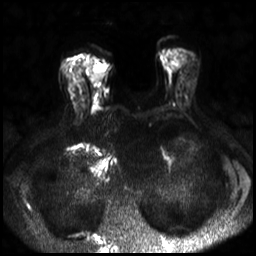
Breast MRI, one axial slice. Slice 11 of 30 in the series (ordered by position). Diffusion-weighted series; image 2 of 4 stored at this slice position (different b-values; order by instance number). 3 T. 4 mm slice thickness. 256 × 256 image matrix. Female patient.
Annotated regions visible in this slice (expert manual segmentation):
- tumour on diffusion-weighted imaging: box from (x=93, y=65) to (x=107, y=83) px